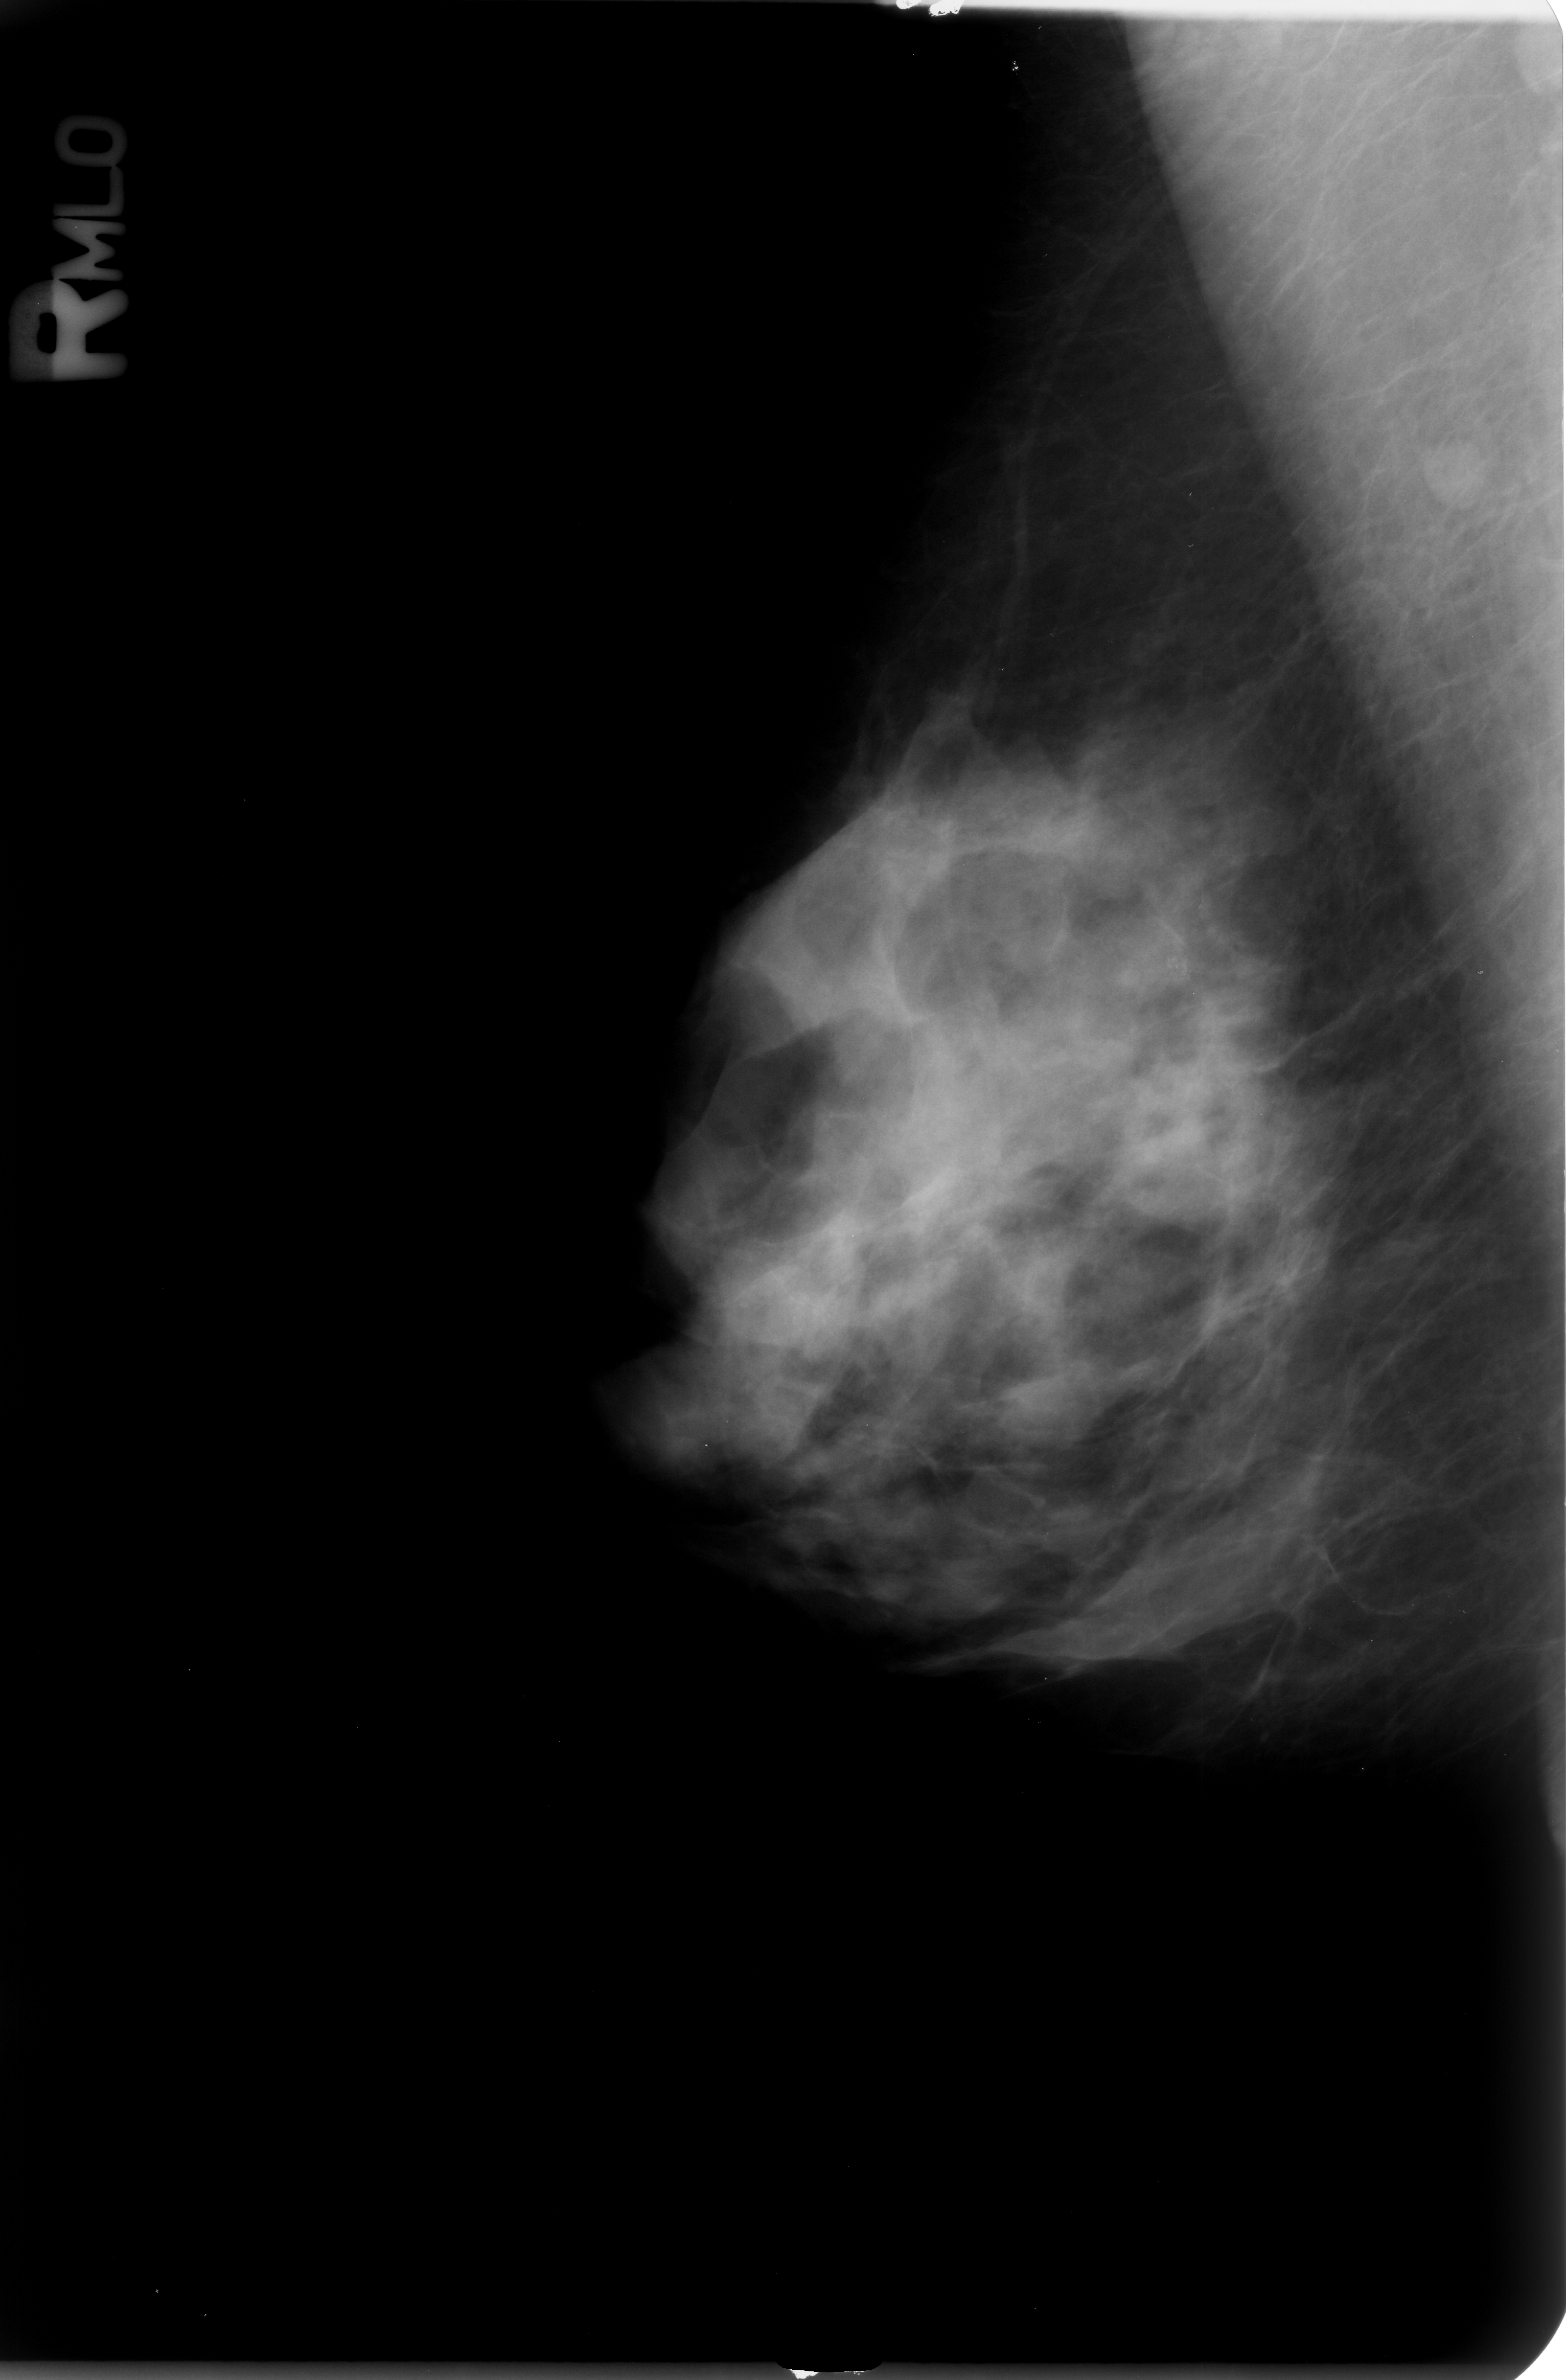
Digitized screen-film mammogram. Right breast. Mediolateral oblique (MLO) view. 1566 × 2380 image matrix.
Marked abnormalities (boxes around the expert regions of interest):
- calcifications, morphology amorphous, distribution clustered; BI-RADS assessment category 3; subtlety rating 3 on a 1 (subtle) to 5 (obvious) scale; pathology (as recorded): benign: bounding box <1128,920,1211,1007> (left, top, right, bottom; pixels)